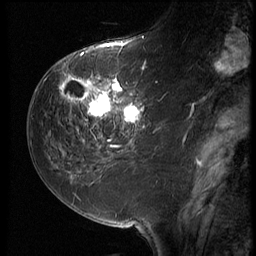
Breast MRI (dynamic contrast-enhanced), one sagittal slice; position 25 of 64 along the scan axis; 3 images stored at this slice position (order not interpretable as contrast timing); 1.5 T; TE 4.2 ms, TR 9 ms; 256 × 256 image matrix, field of view 180 × 180 mm. Female patient, age 59 years. Case-level facts recorded for this patient, not image findings: setting: breast cancer imaged before/during neoadjuvant chemotherapy; receptor status: HER2-positive.
Structures marked on this image (semi-automatic segmentation, software-assisted and operator-edited):
- analysis volume of interest (the breast-tissue region the enhancement analysis was run in; not a lesion): bounding box <54,65,155,132> (left, top, right, bottom; pixels)
- tumour enhancement mask (voxels above the 140 % enhancement threshold inside the analysis volume of interest): <61,65,146,128>